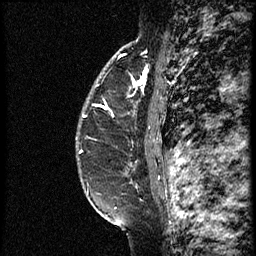
Breast MRI (dynamic contrast-enhanced), one sagittal slice; slice 45 of 60 in the series (ordered by position); dynamic contrast-enhanced study with each time point stored as its own series, time point 2 of 3 at this slice position (early post-contrast, ordered by acquisition time); 1.5 T; TE 4.2 ms, TR 18.9 ms; 2 mm slice thickness; 256 × 256 image matrix. Female patient. Case-level facts recorded for this patient, not image findings: setting: breast cancer imaged before/during neoadjuvant chemotherapy; receptor status: HER2-positive.
Structures marked on this image (semi-automatic segmentation, software-assisted and operator-edited):
- analysis volume of interest (the breast-tissue region the enhancement analysis was run in; not a lesion): bounding box [x1, y1, x2, y2] px = [77, 64, 161, 147]
- tumour enhancement mask (voxels above the 100 % enhancement threshold inside the analysis volume of interest): [83, 81, 140, 118]